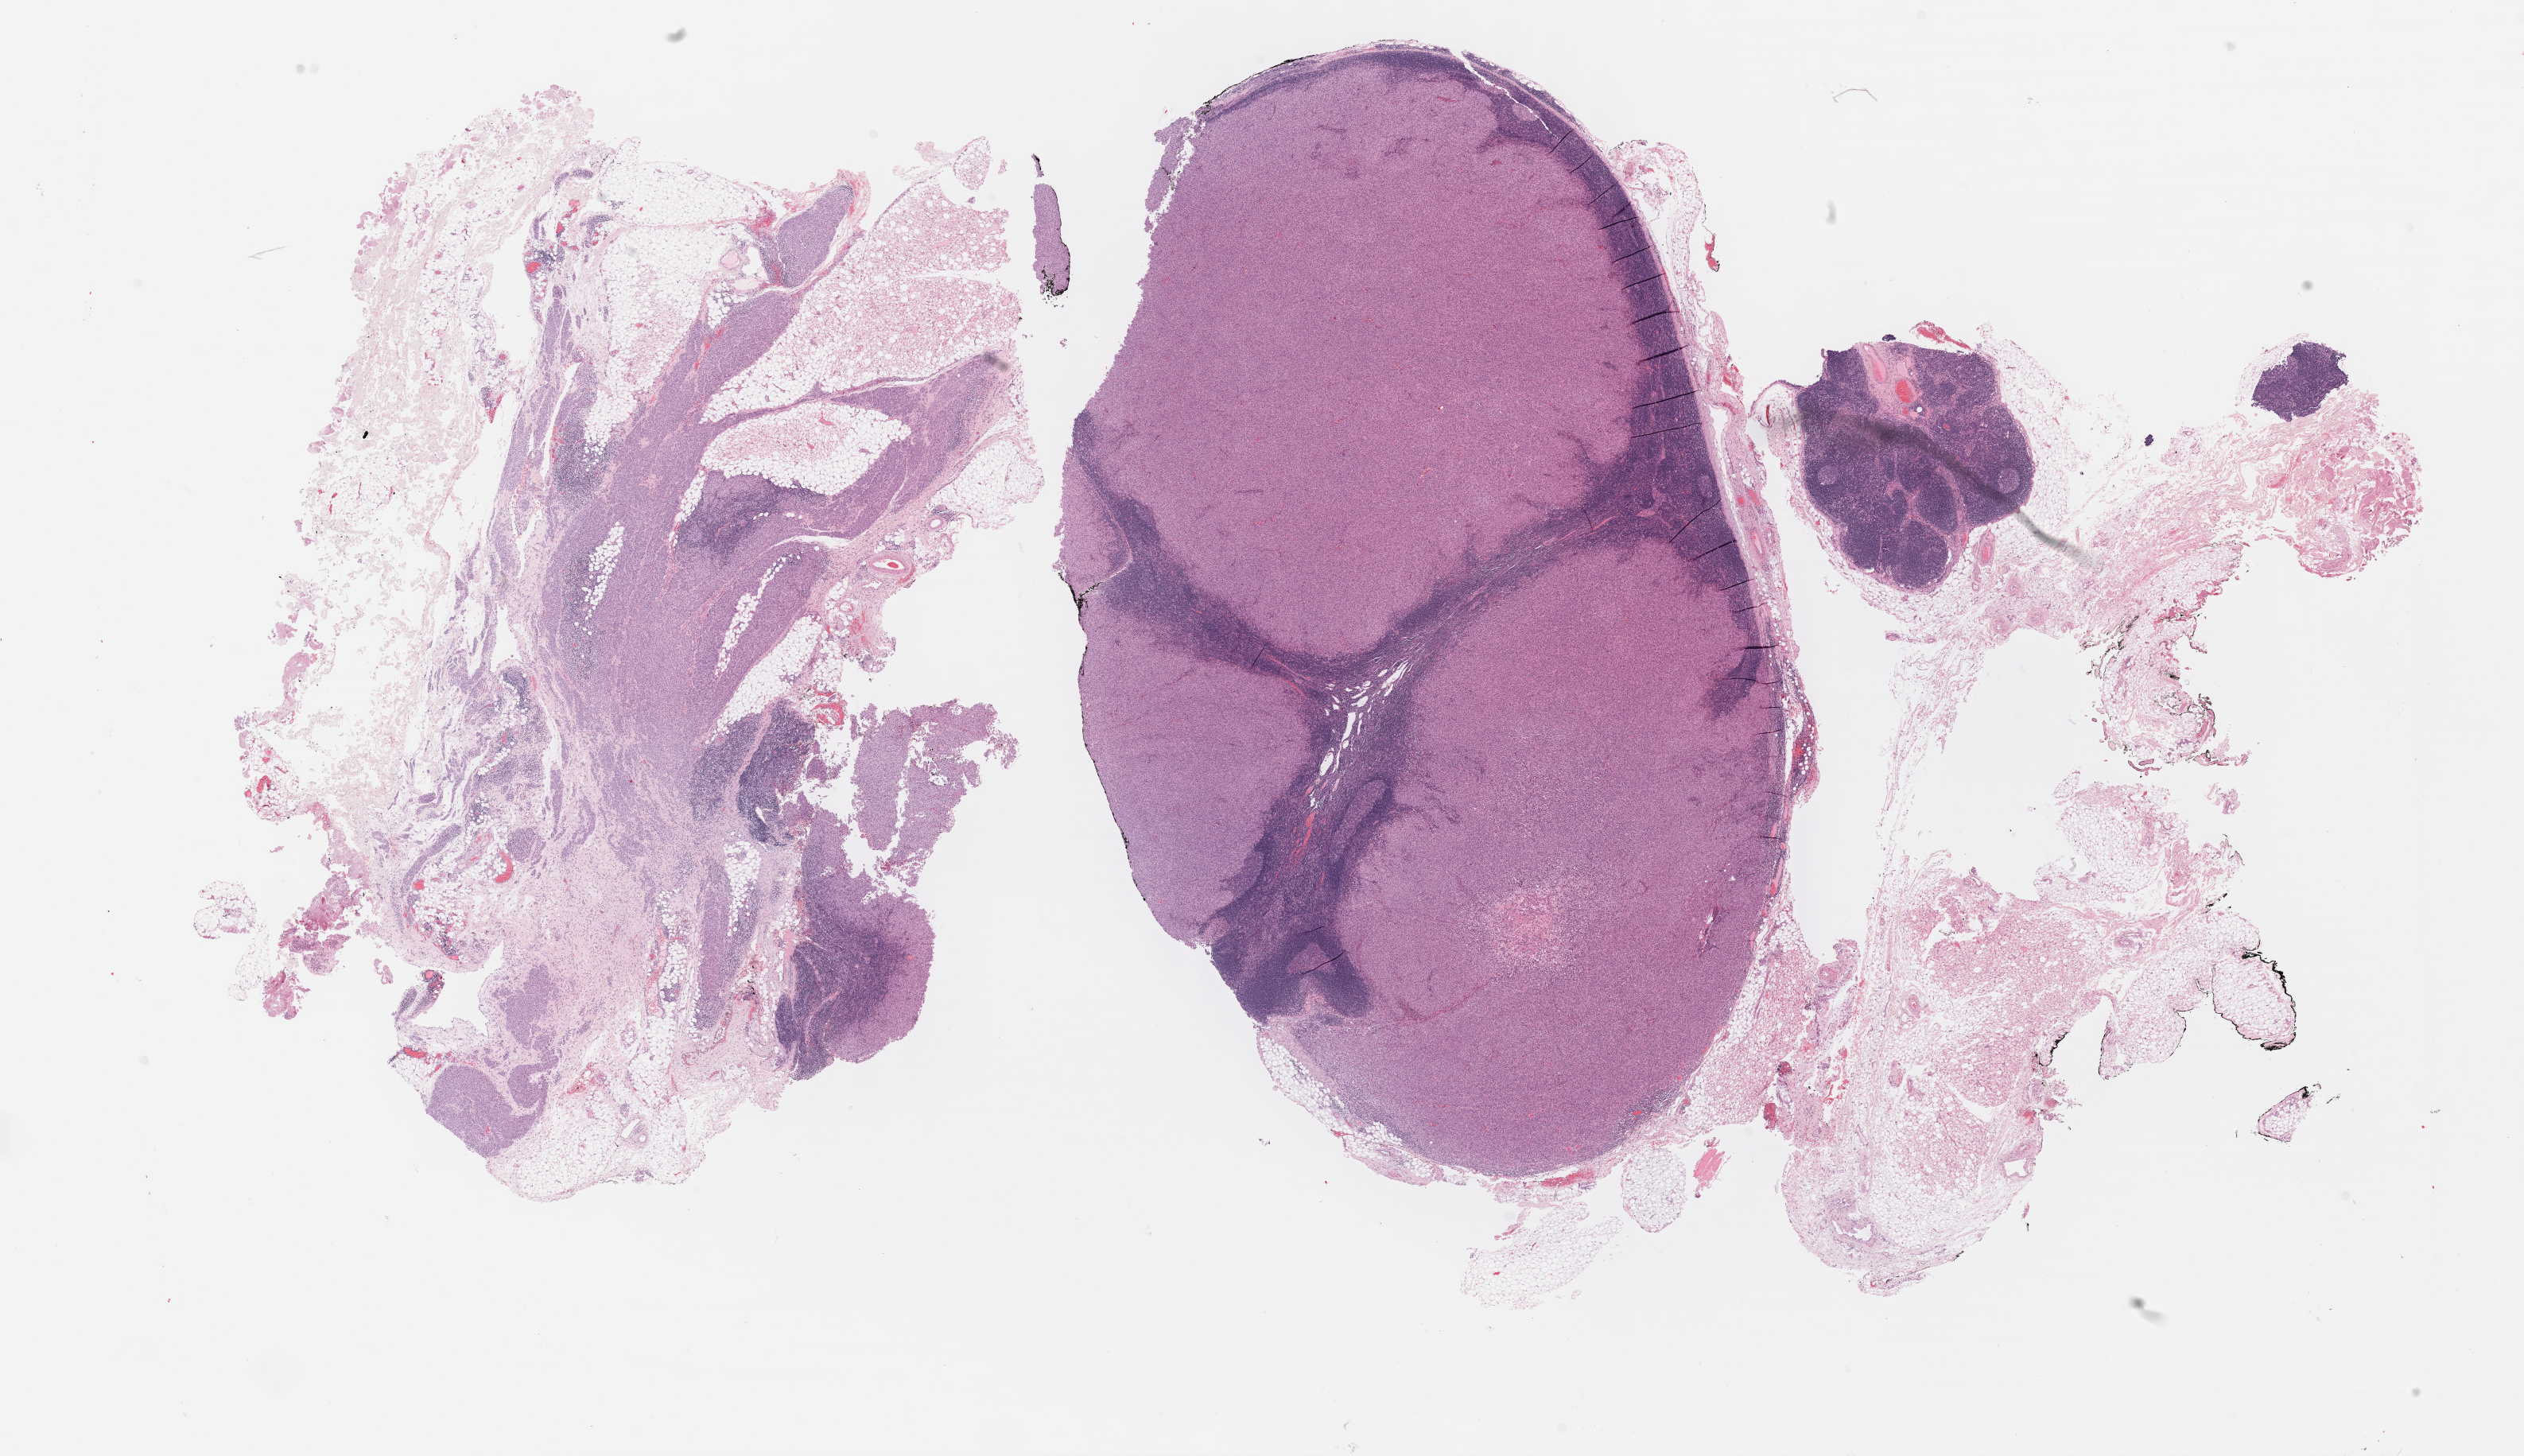
Whole-slide histology image, H&E-stained, low-resolution overview of the scanned area, about 25.7 x 14.8 mm, FFPE section, metastatic tumour sample, sampled site: lymph nodes of axilla or arm. Female patient; age at initial diagnosis 25 years.
This section: metastatic tumour tissue. Patient diagnosis: Malignant melanoma, NOS.